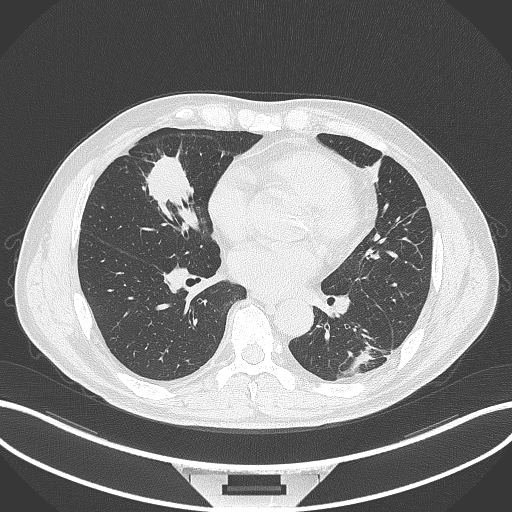
Chest CT, one axial slice; position 128 of 399 along the scan axis; reconstruction kernel B70f; lung window (W 1500 / L -600 HU); 1 mm slice thickness; 512 × 512 image matrix, field of view 400 × 400 mm. Patient: male, 59 years. Case-level facts recorded for this patient, not image findings: clinical TNM (as recorded): T2a N1 M0.
Structures marked on this image (bounding box drawn by a radiologist):
- lung tumour (recorded histology: adenocarcinoma): bounding box [x1, y1, x2, y2] px = [139, 143, 199, 207]